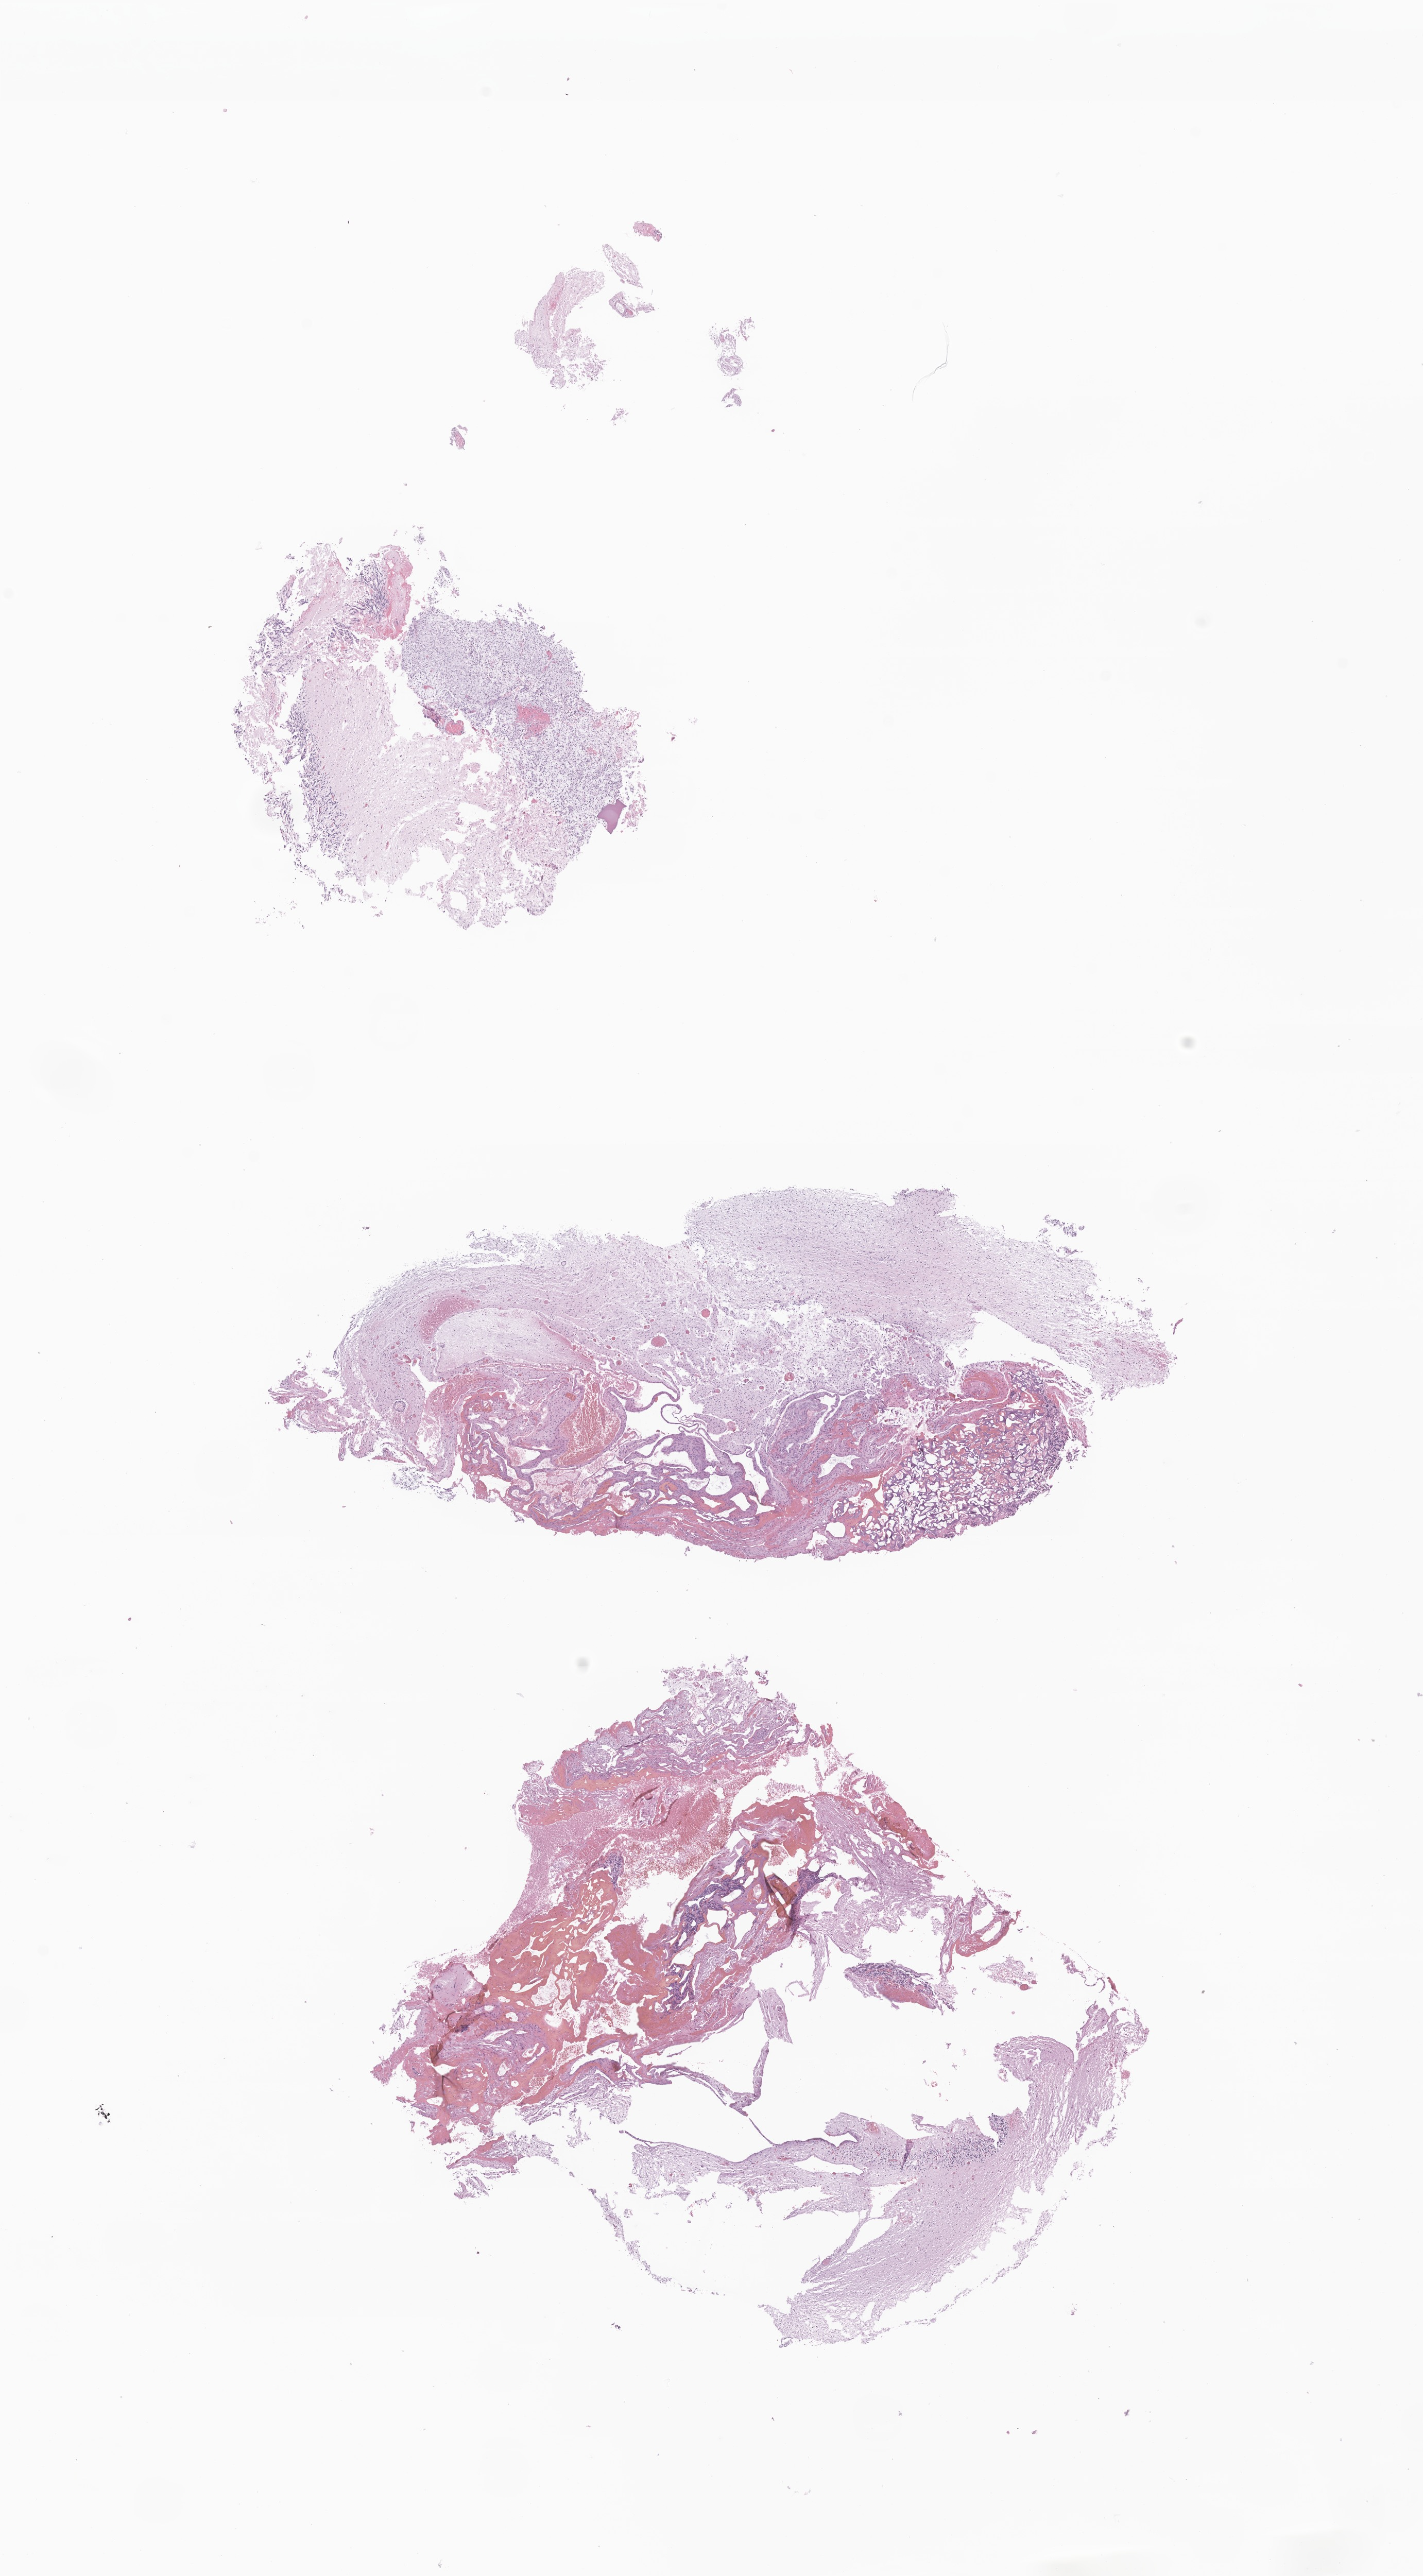
Whole-slide image, haematoxylin and eosin stain of tumor tissue from the cerebral ventricle, low-resolution overview of the scanned area, about 11.6 x 21.1 mm, FFPE section. Female patient, age 163 months (13 years 7 months).
Diagnosis: Pilocytic astrocytoma.